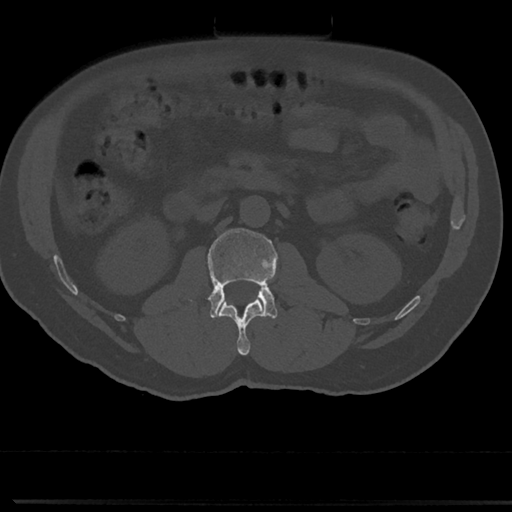
CT including the spine, one axial slice. Position 39 of 817 along the scan axis. Reconstruction kernel Br40s/3. 120 kVp. Bone window (W 1800 / L 400 HU). 0.5 mm slice thickness. 512 × 512 image matrix. Patient: male, 61 years. From the clinical record (not read from this slice): primary cancer: prostate.
Outlined on this slice (semi-automatically segmented with operator editing):
- L1 vertebra: bounding box [x1, y1, x2, y2] px = [219, 299, 263, 355]
- L2 vertebra: [207, 228, 277, 318]